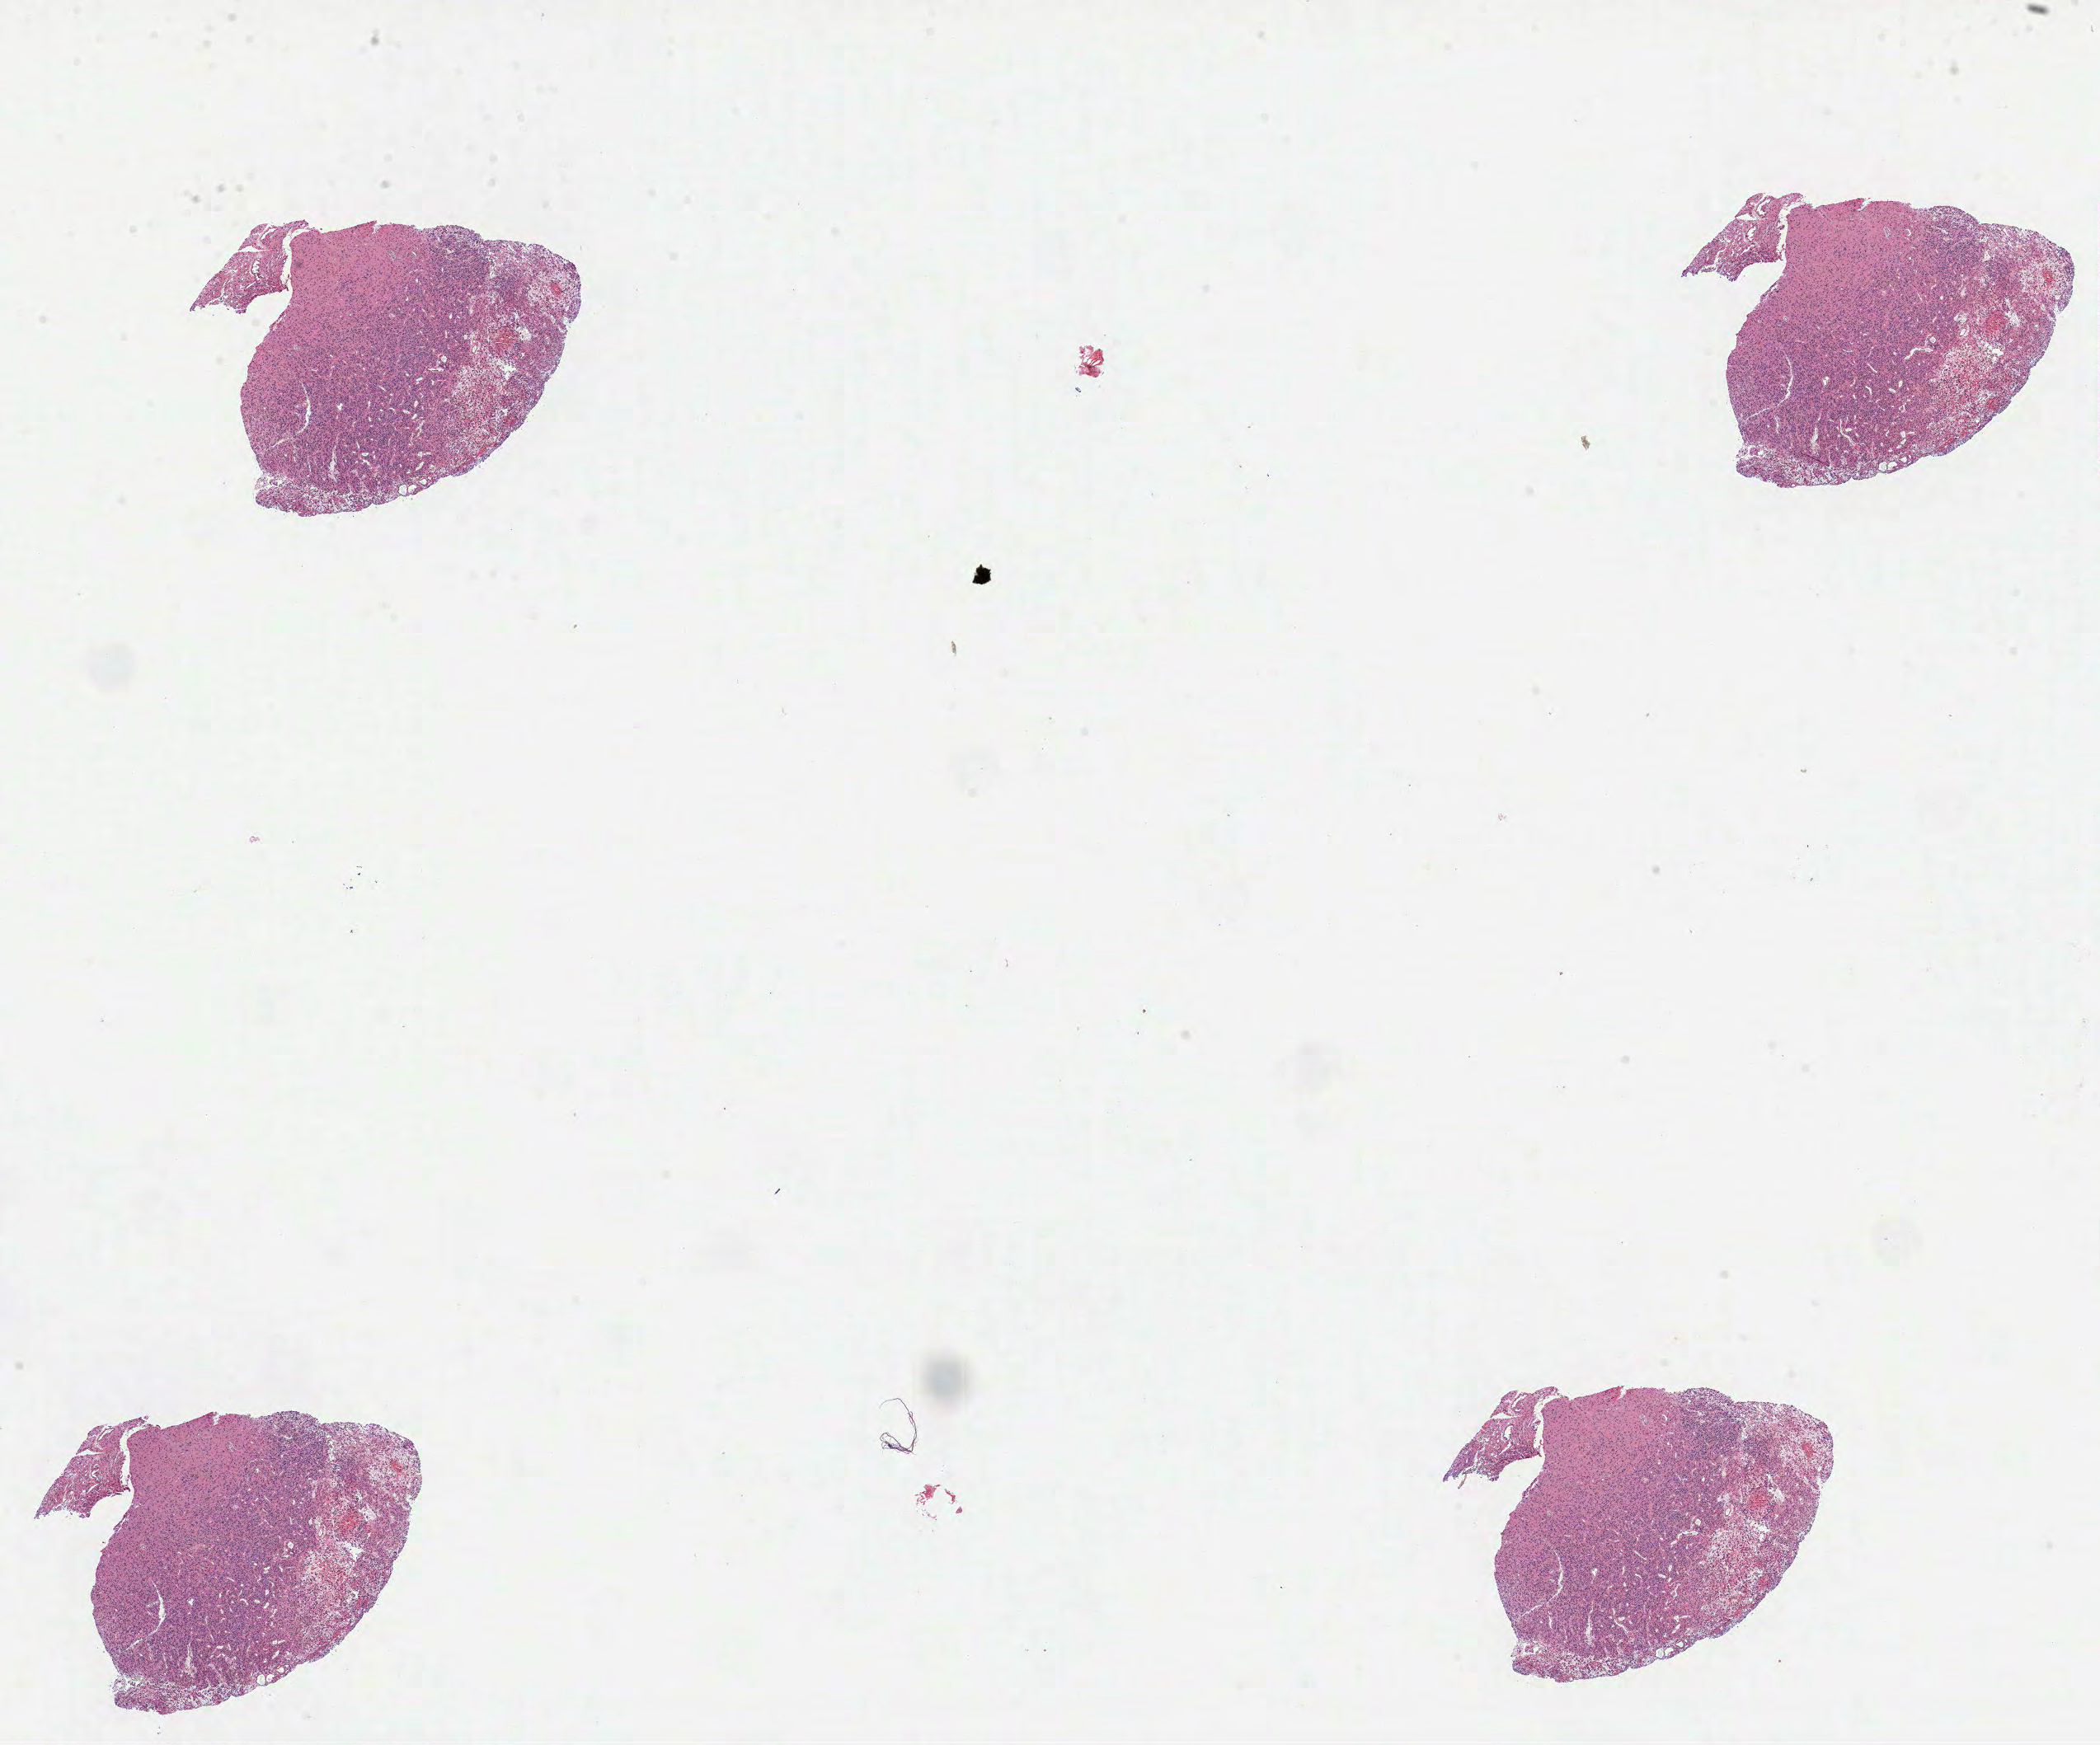
Digitized H&E-stained tissue section (whole slide), low-resolution overview of the scanned area, about 20.5 x 17.1 mm. Formalin-fixed paraffin-embedded (FFPE) diagnostic section. Brain, primary tumour sample. Patient: male, age at initial diagnosis 45 years. Histologic grade: G3 (poorly differentiated).
* pathologic diagnosis: Oligodendroglioma, anaplastic (cerebrum)